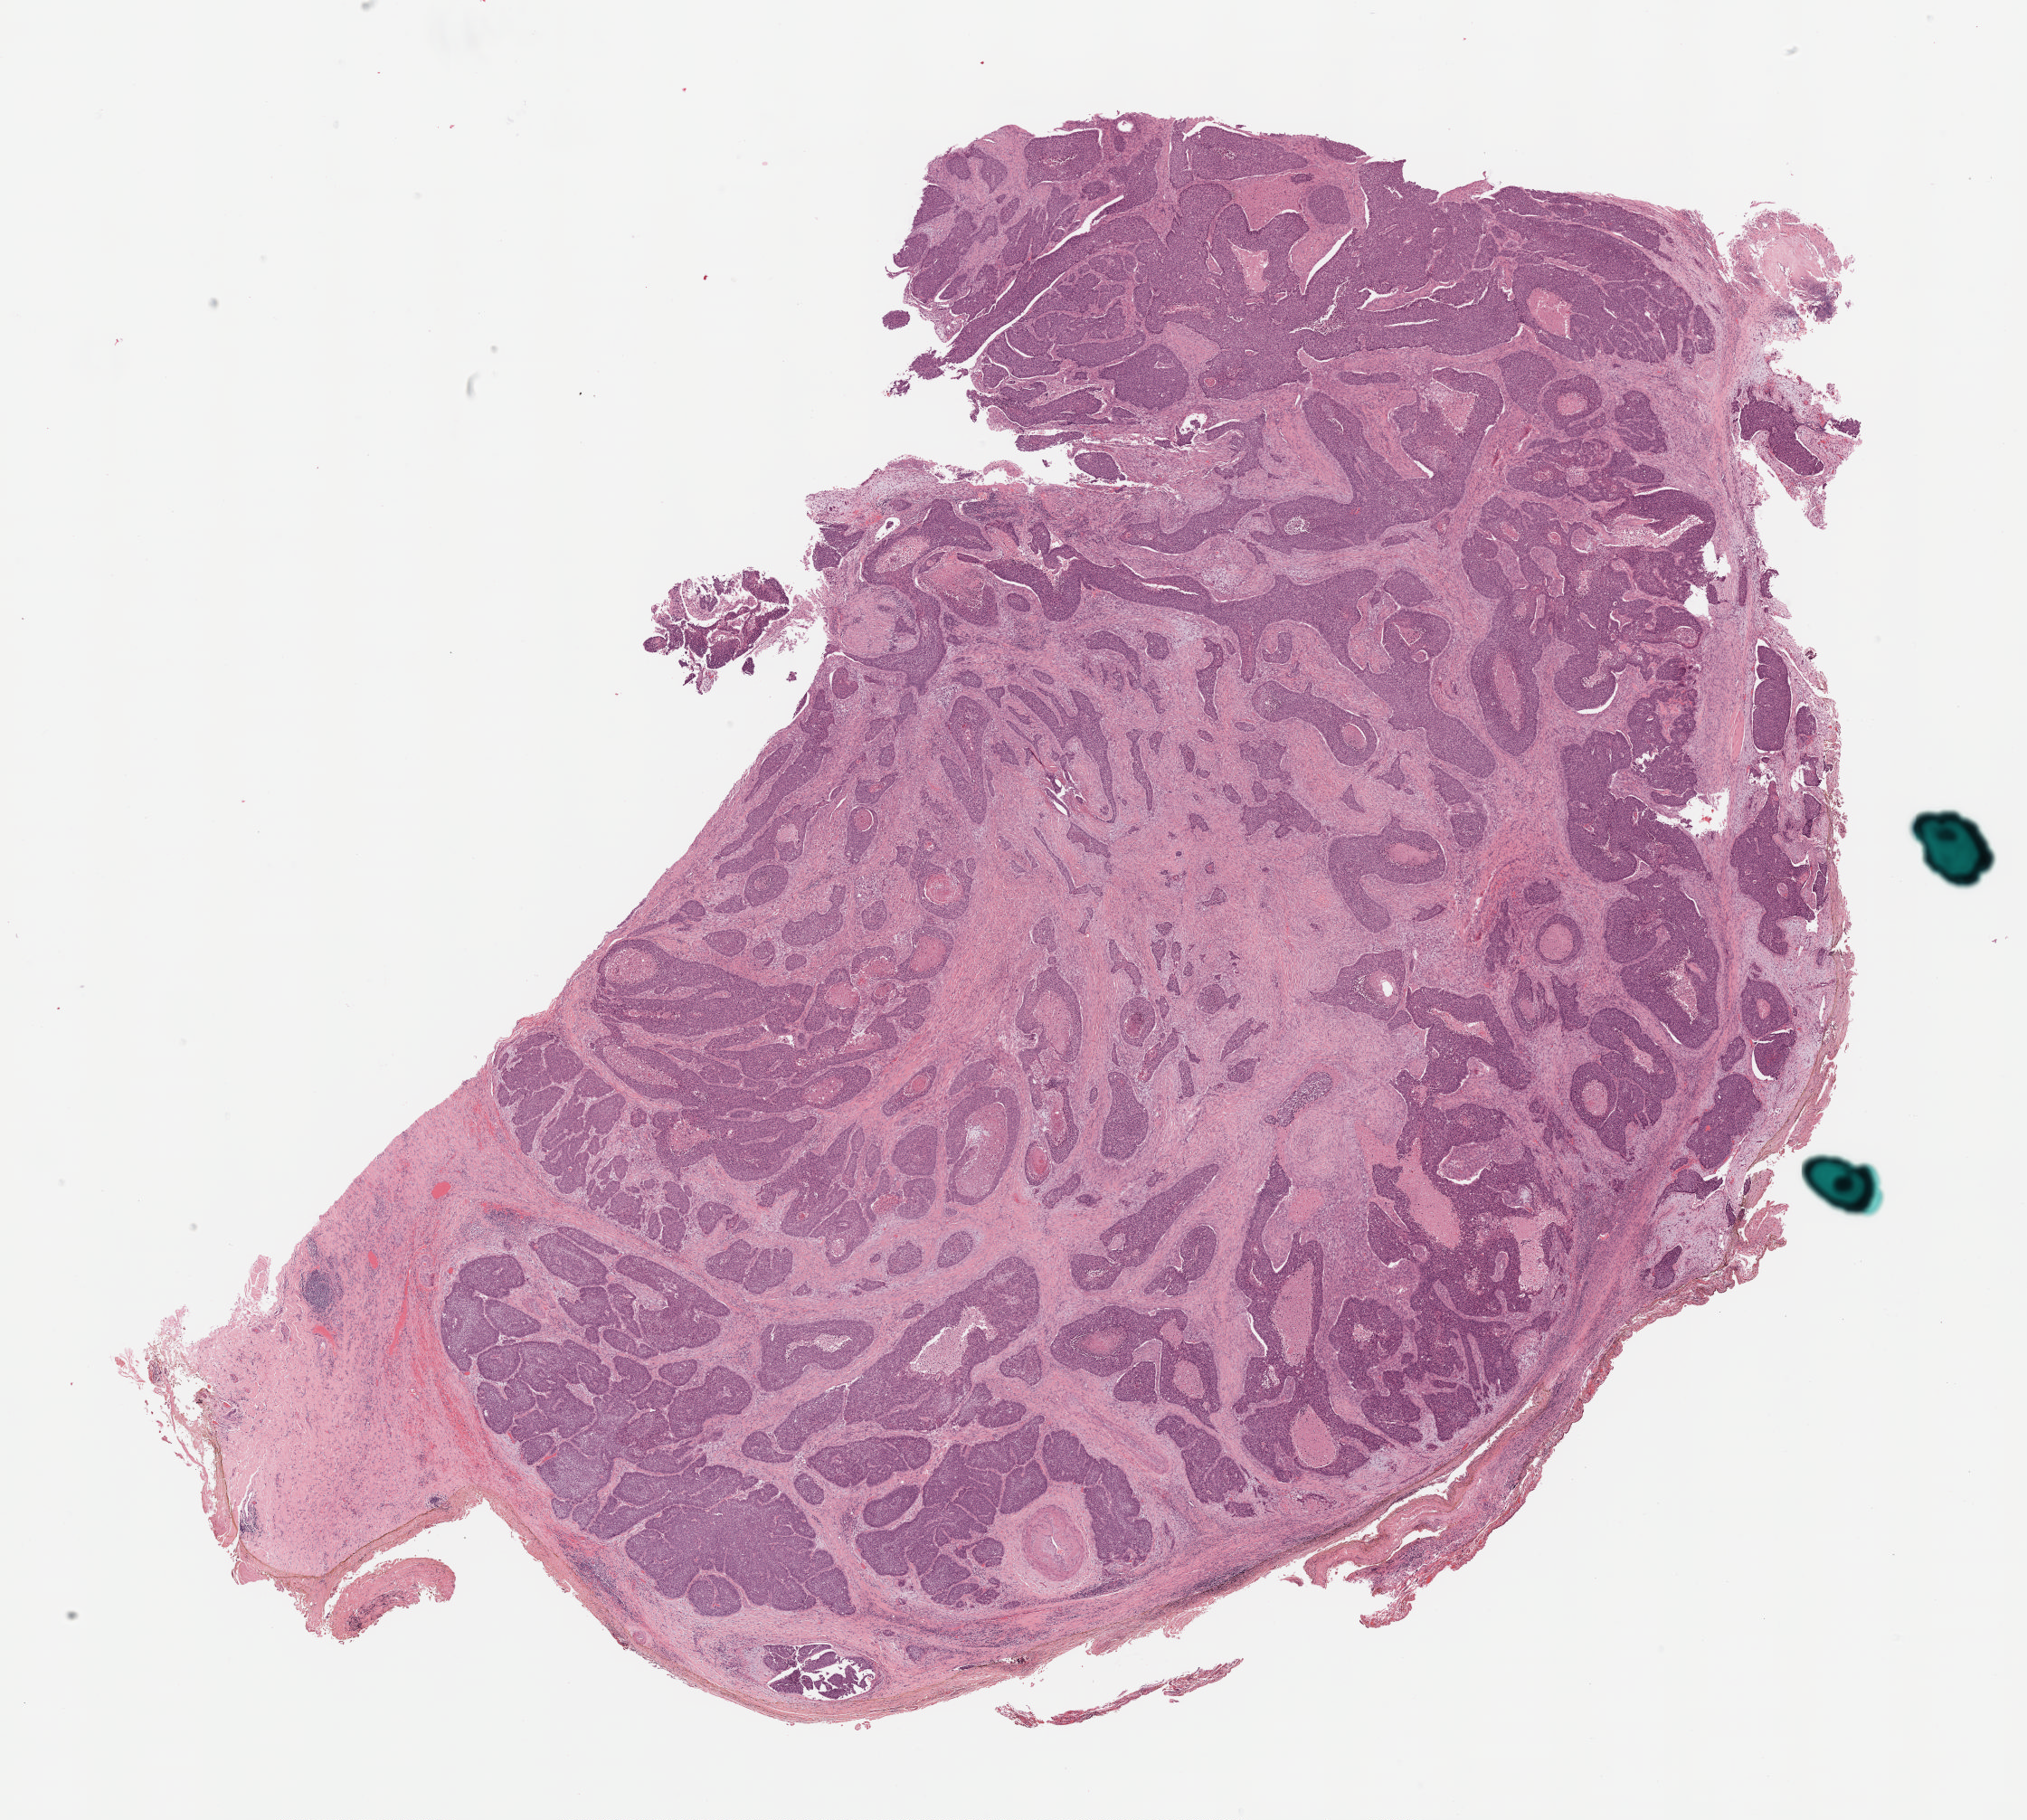
H&E-stained whole-slide image — low-resolution overview of the scanned area, about 18.0 x 16.1 mm; formalin-fixed paraffin-embedded (FFPE) diagnostic section; sample: primary tumour, head and neck. Male patient; age at initial diagnosis 73 years. Histologic grade: G3 (poorly differentiated).
Lymph nodes positive (case pathology): 1 of 49 examined. Laterality: right. AJCC pathologic stage: III. Pathologic diagnosis: Basaloid squamous cell carcinoma (cheek mucosa).